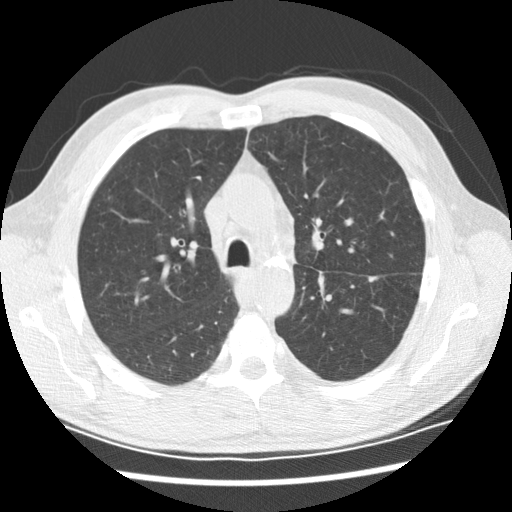
Low-dose screening chest CT, one axial slice; slice 139 of 208 in the series (ordered by position); reconstruction kernel STANDARD; 120 kVp; lung window (W 1500 / L -600 HU); 2.5 mm slice thickness; 512 × 512 image matrix, field of view 340 × 340 mm.
Outlined on this slice (outlined manually by an expert reader):
- lesion 2 (tumor, lower lobe of left lung): bounding box (x1, y1, x2, y2) in pixels: (368, 276, 377, 283)